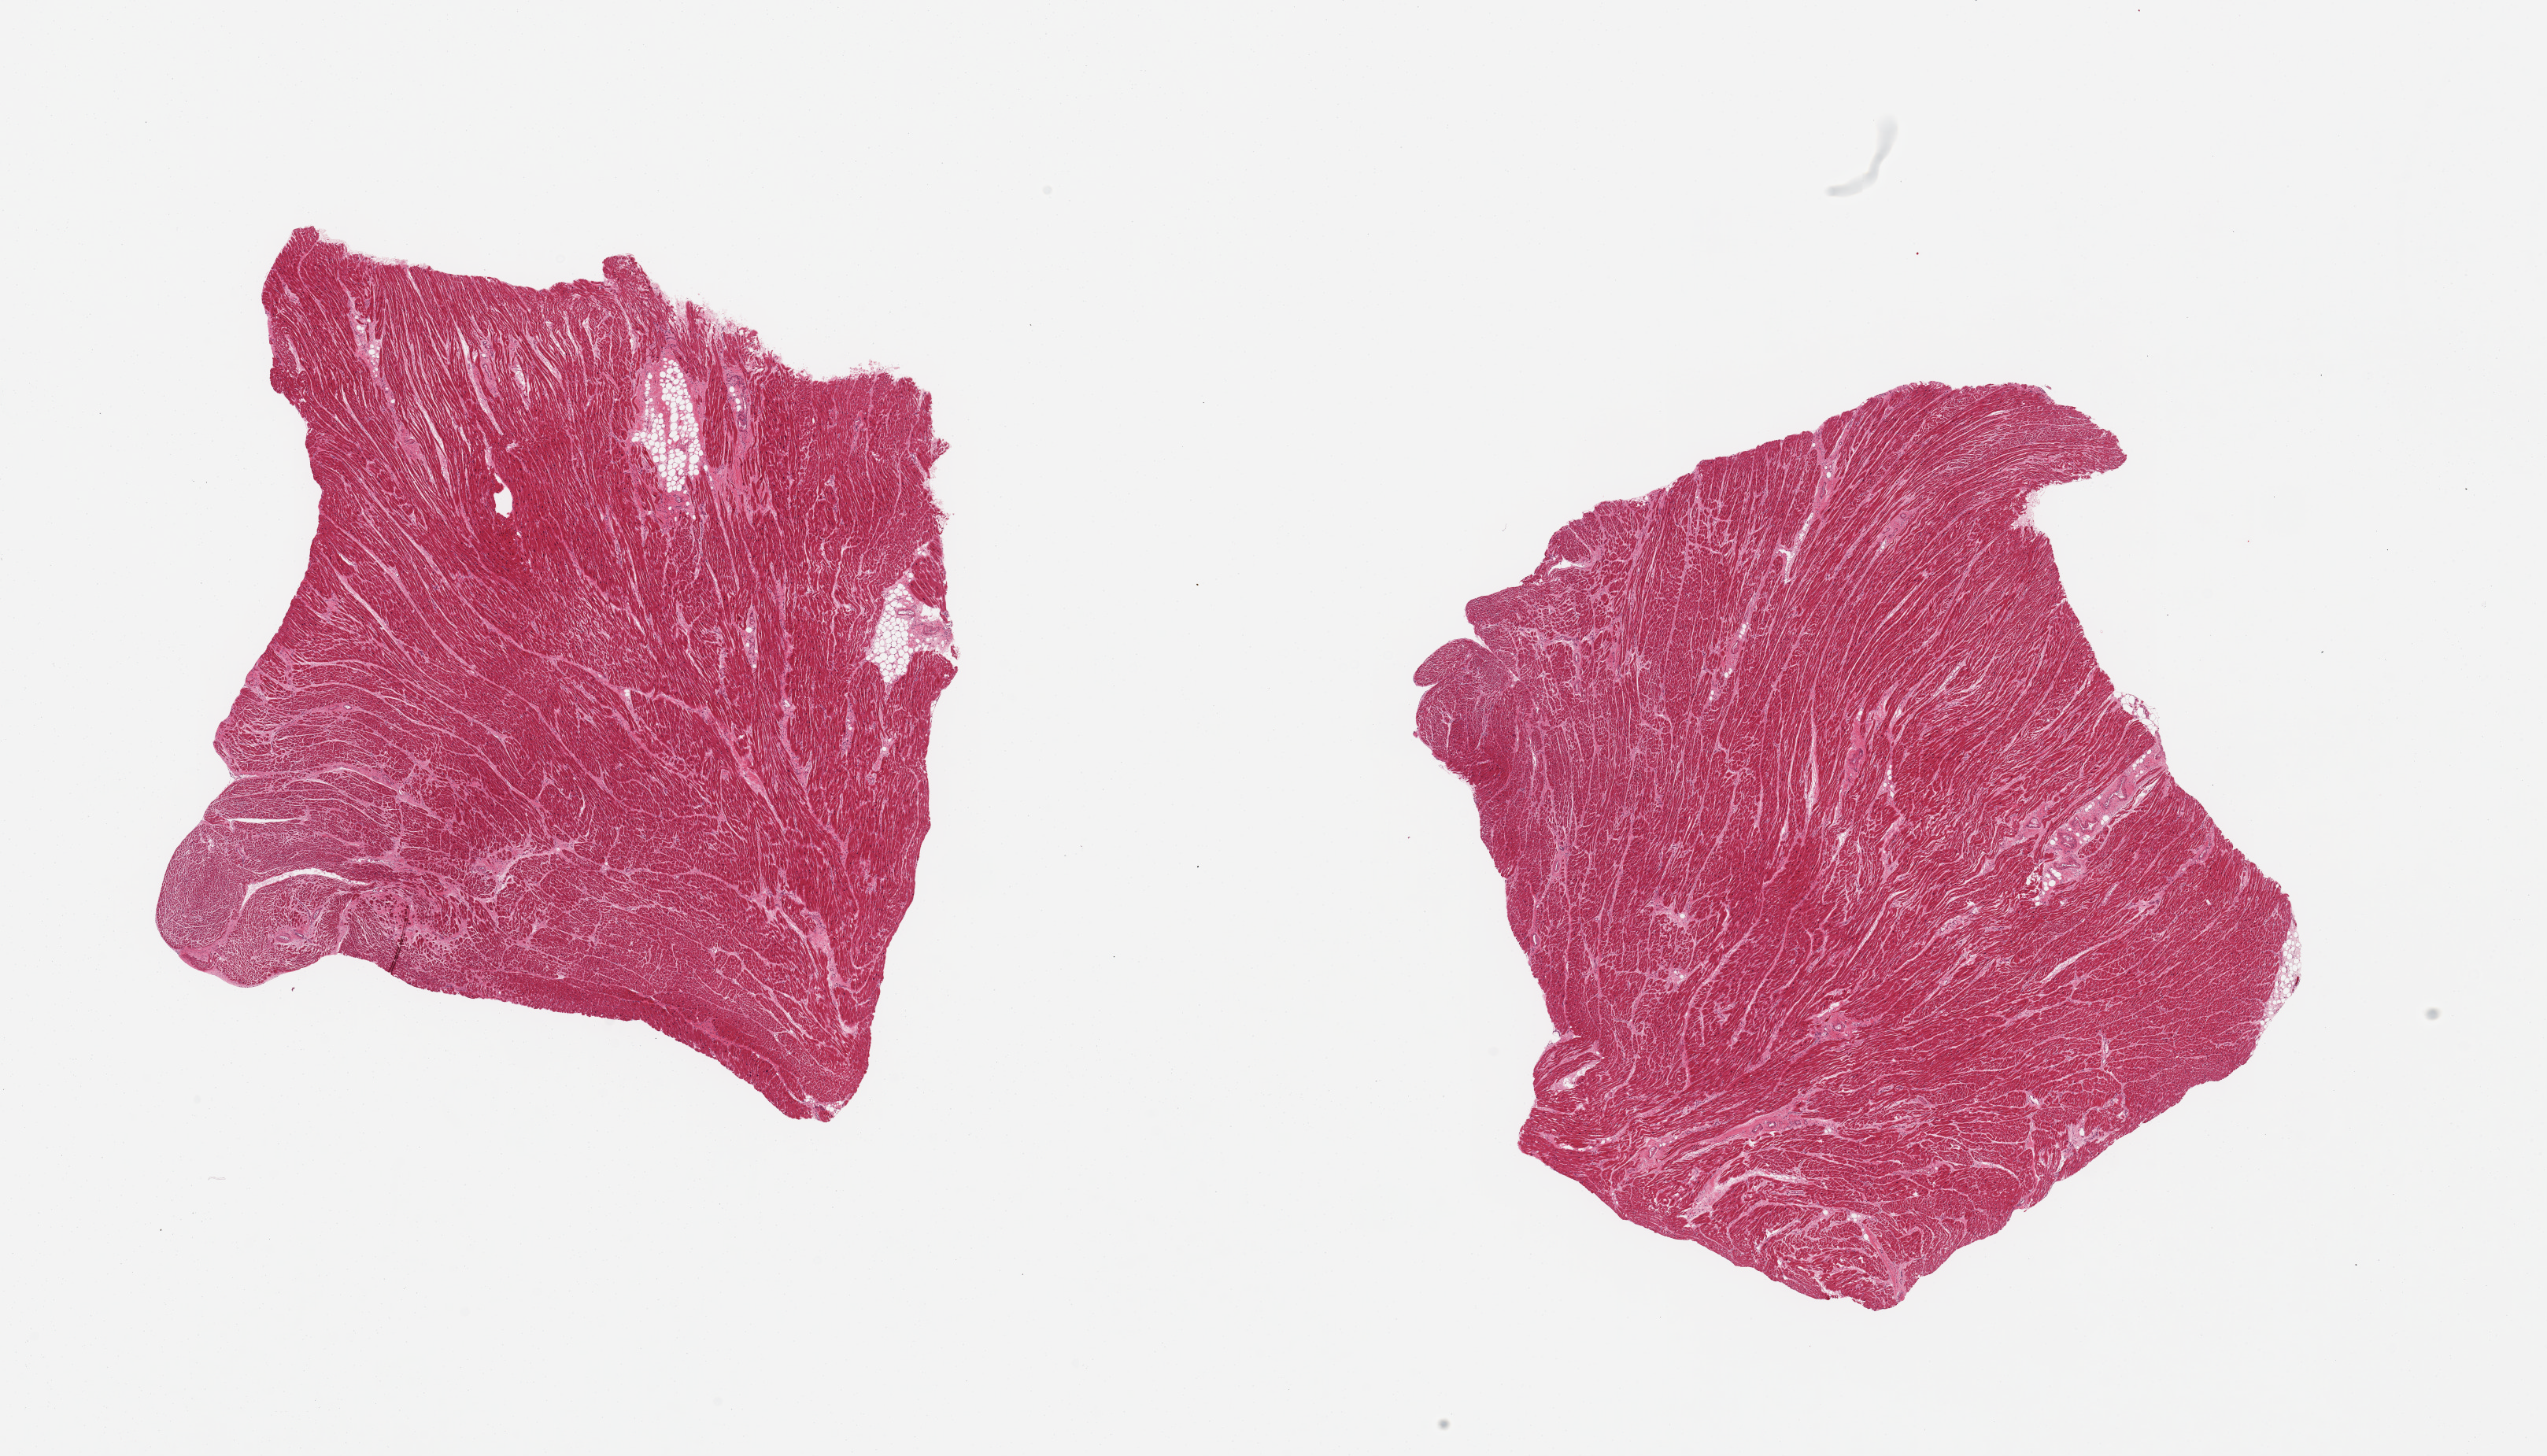
Whole-slide image, haematoxylin and eosin stain, low-resolution overview of the scanned area, about 25.6 x 14.6 mm, PAXgene-fixed, paraffin-embedded tissue, sampled site (target tissue): heart, donor tissue sample. Male donor.
- pathologist's review note for this sample: 2 pieces; 1 has 10% internal fat